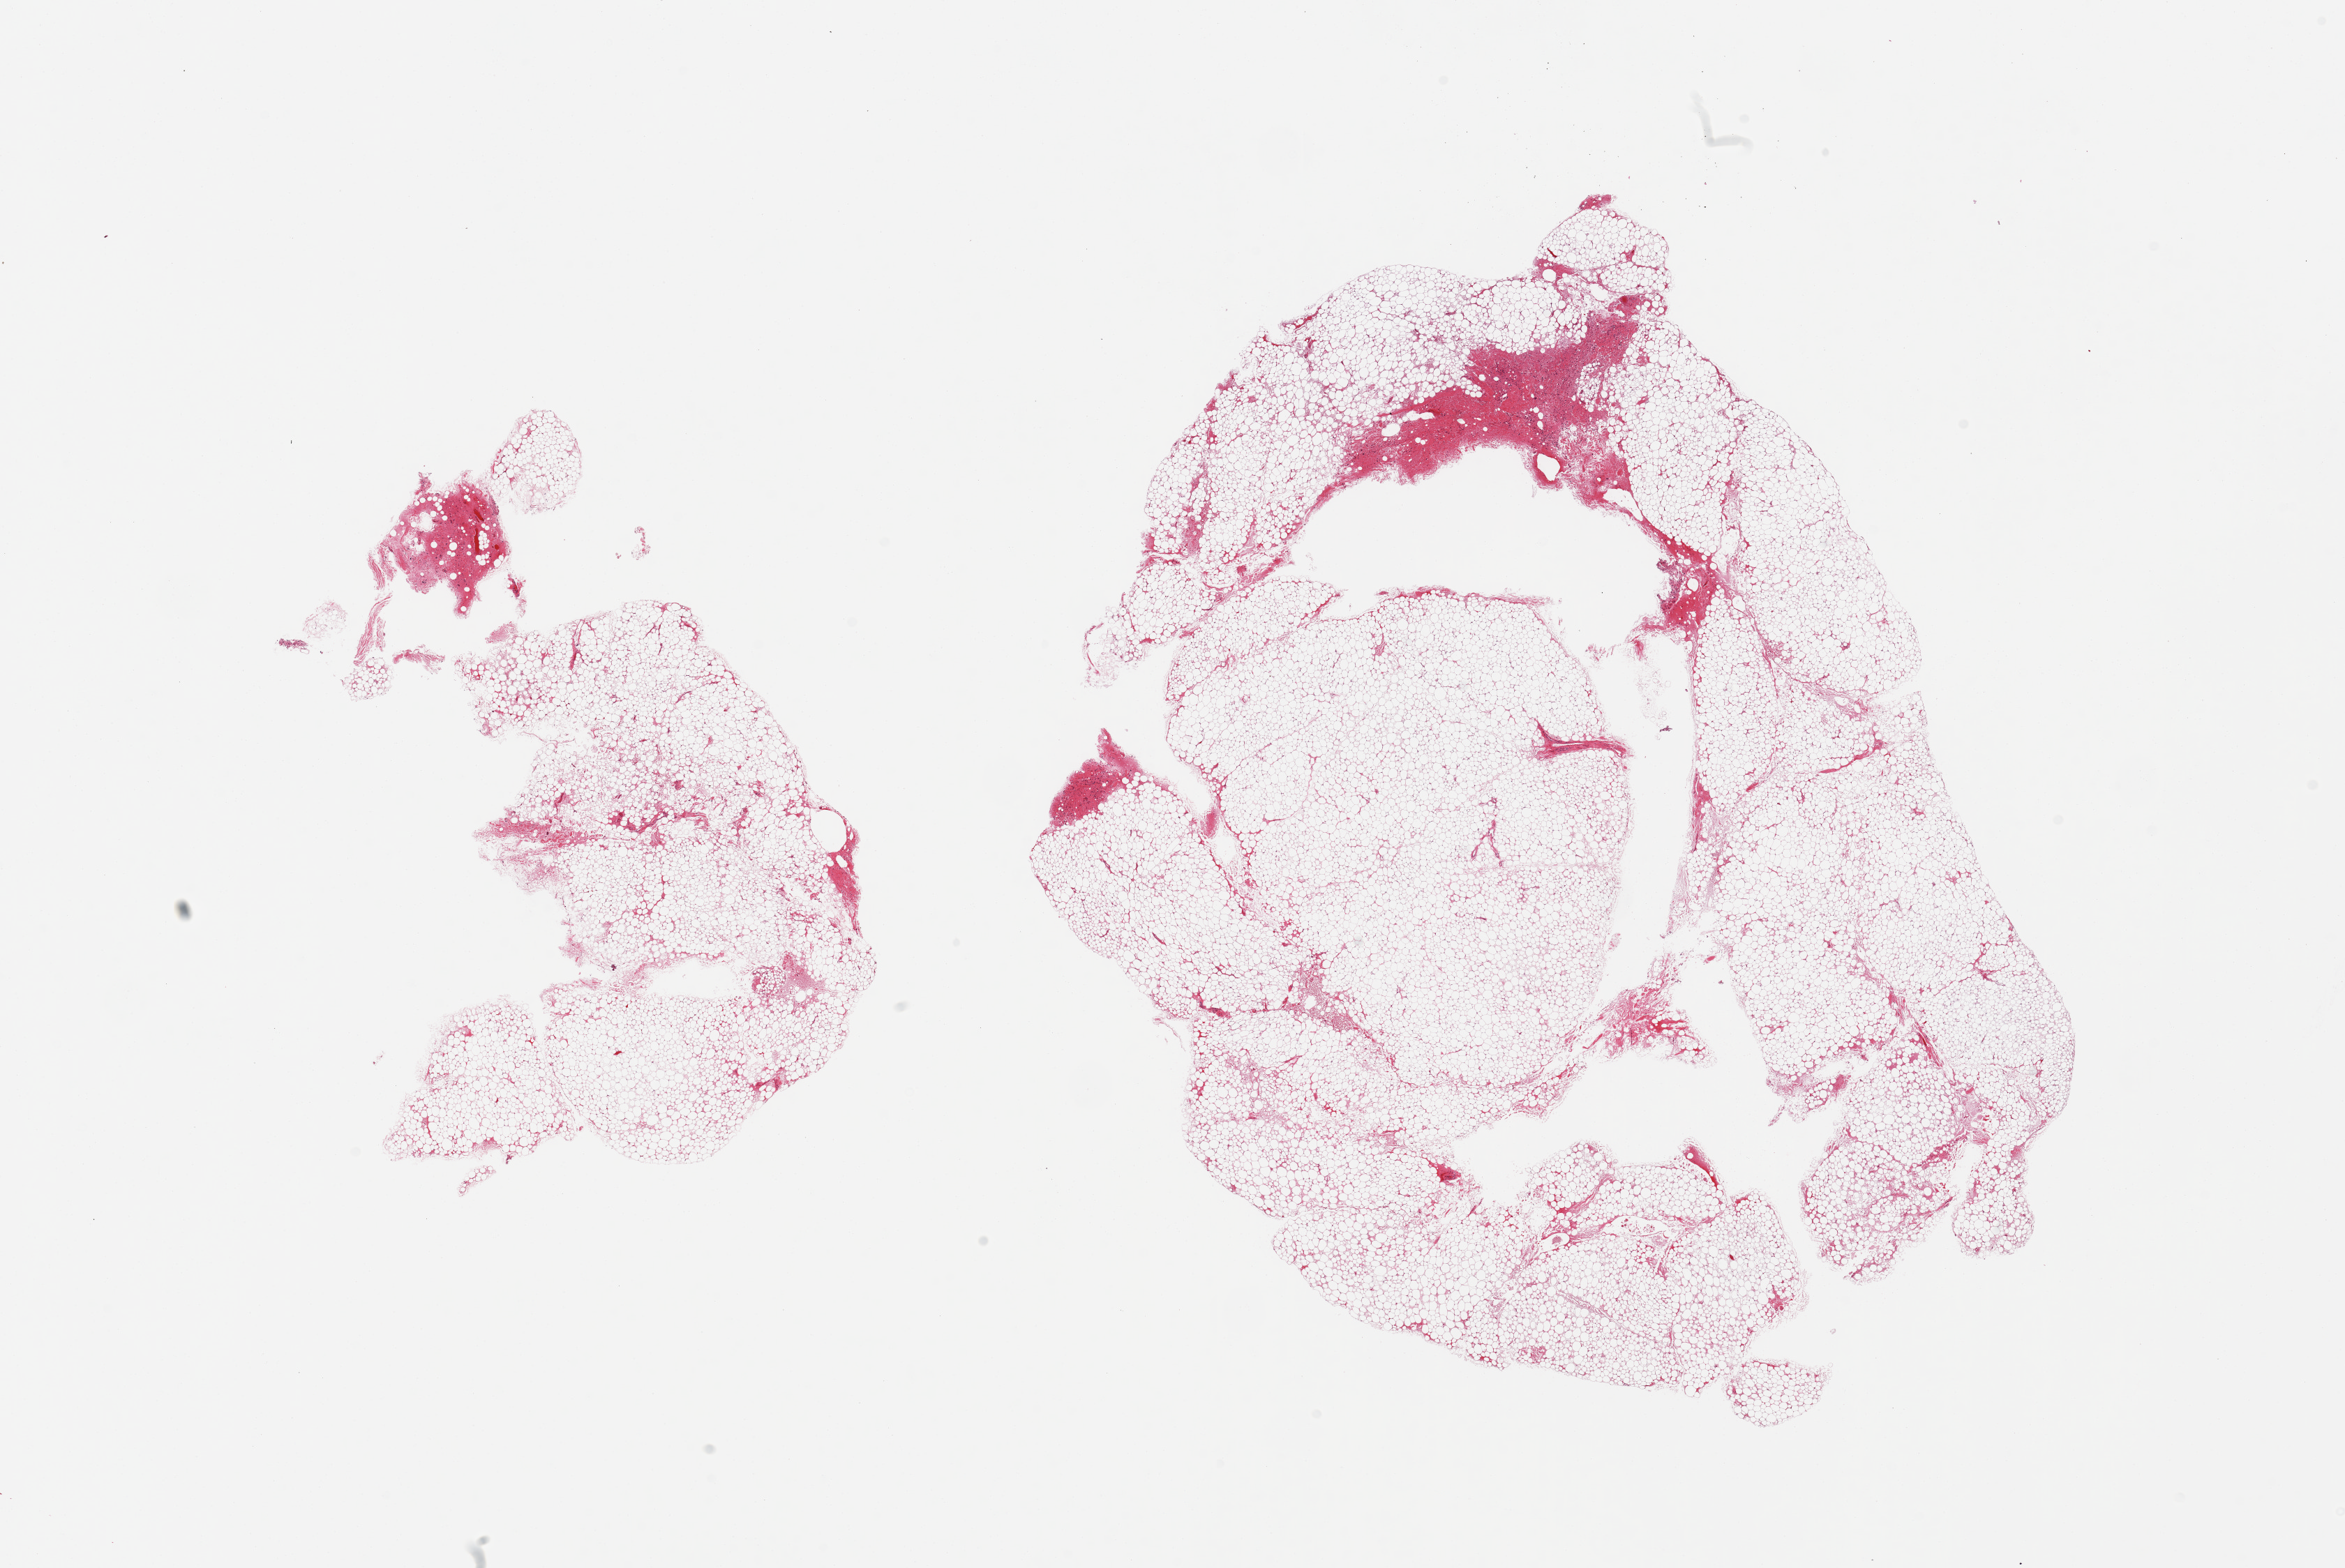
H&E whole-slide image, brightfield, whole scanned area (about 26.6 x 17.8 mm, acquisition: 20x scan) shown as a low-resolution overview, PAXgene-fixed paraffin-embedded (PFPE) section, sampled site (target tissue): adrenal gland, tissue donor sample. Male donor.
Reviewer comment on this tissue sample: 2 pieces; adipose tissue only.